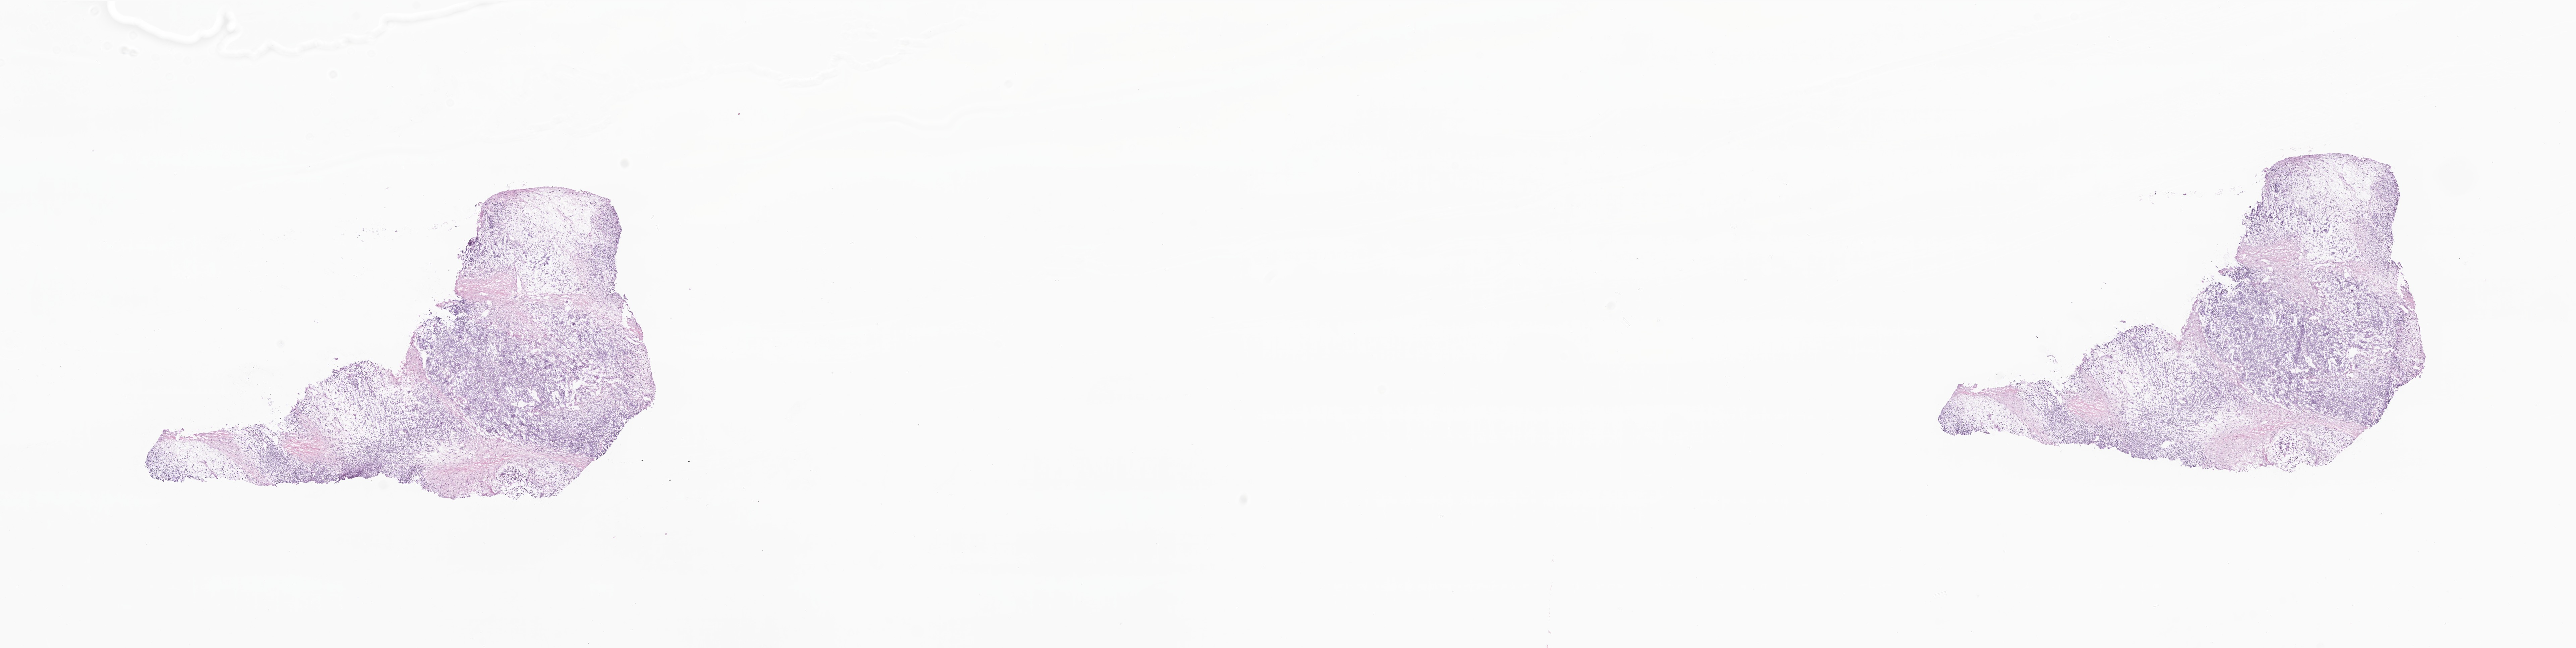
Whole-slide image, haematoxylin and eosin stain — low-resolution overview of the scanned area, about 32.4 x 8.1 mm. Frozen section. Specimen: primary tumor. Anatomic site: body of pancreas. Female patient; age at initial diagnosis 71 years. Tumor grade: G3 (poorly differentiated). Slide review estimates, as recorded: tumor cells 75%, tumor nuclei 95%, stromal cells 19%, necrosis 2%, normal cells 4%. Inflammatory infiltration, as recorded: lymphocyte infiltration 0%, monocyte infiltration 0%, neutrophil infiltration 0%.
AJCC pathologic stage: Stage III. Histologic diagnosis: Carcinosarcoma, NOS.